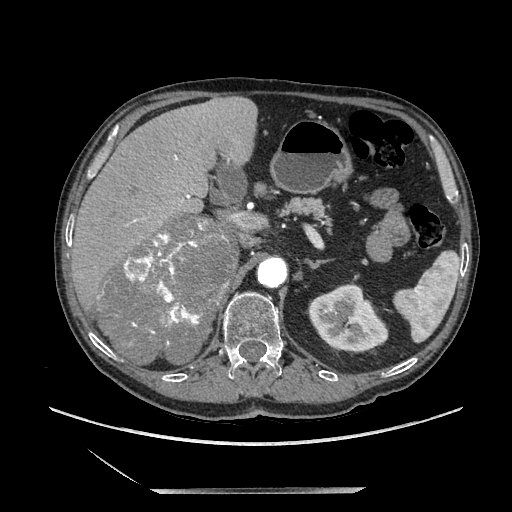
Contrast-enhanced abdominal CT, one axial slice. Slice 130 of 243 in the series (ordered by position). Soft-tissue window (W 400 / L 40 HU). 1.25 mm slice thickness. 512 × 512 image matrix, field of view 420 × 420 mm. Male patient. From the clinical record (not read from this slice): diagnosis: adrenocortical carcinoma; tumour side: right adrenal; tumour size at pathology: 16 cm; Ki-67 index: 17 %; stage (as recorded): 3.
Structures marked on this image (semi-automatic segmentation, software-assisted and operator-edited):
- mass: box from (x=100, y=215) to (x=238, y=364) px